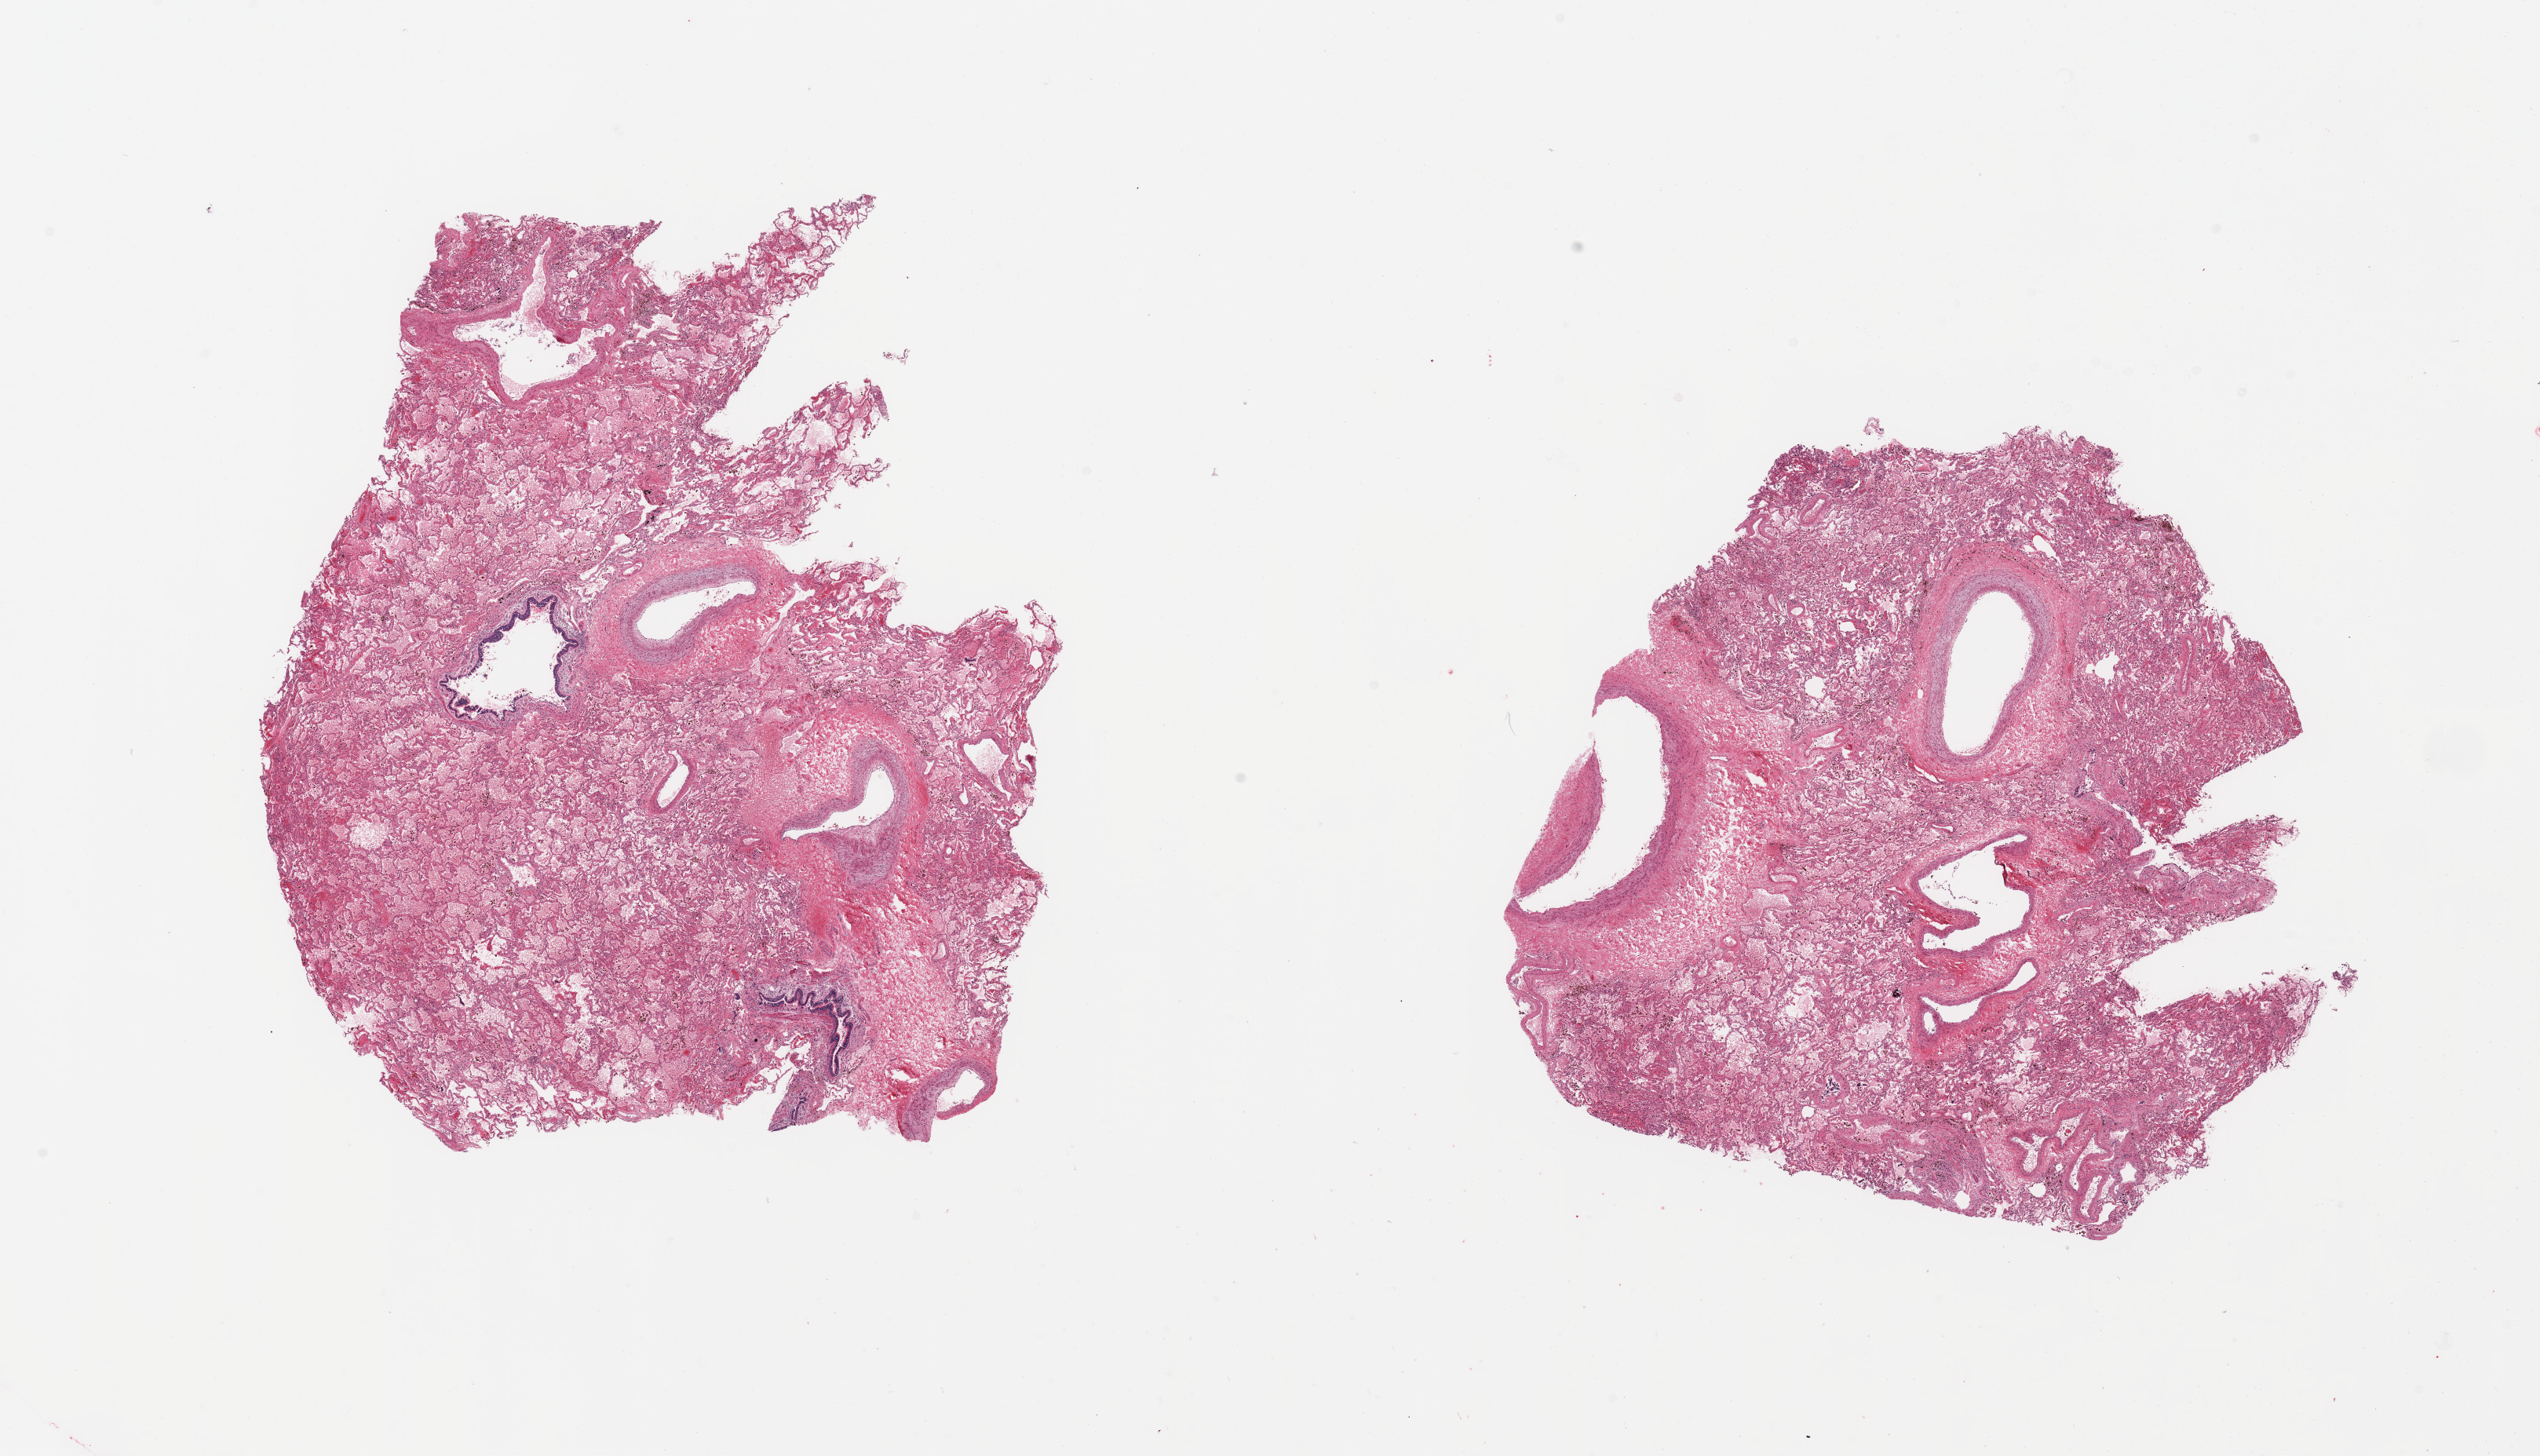
Haematoxylin and eosin whole-slide image, whole scanned area (about 25.6 x 14.7 mm) shown as a low-resolution overview, PAXgene-fixed paraffin-embedded (PFPE) section, sampled site (target tissue): lung, tissue donor sample. Male donor.
• pathologist's review note for this sample: 2 pieces; marked congestion; thick walled large vessels; couple of bronchioles